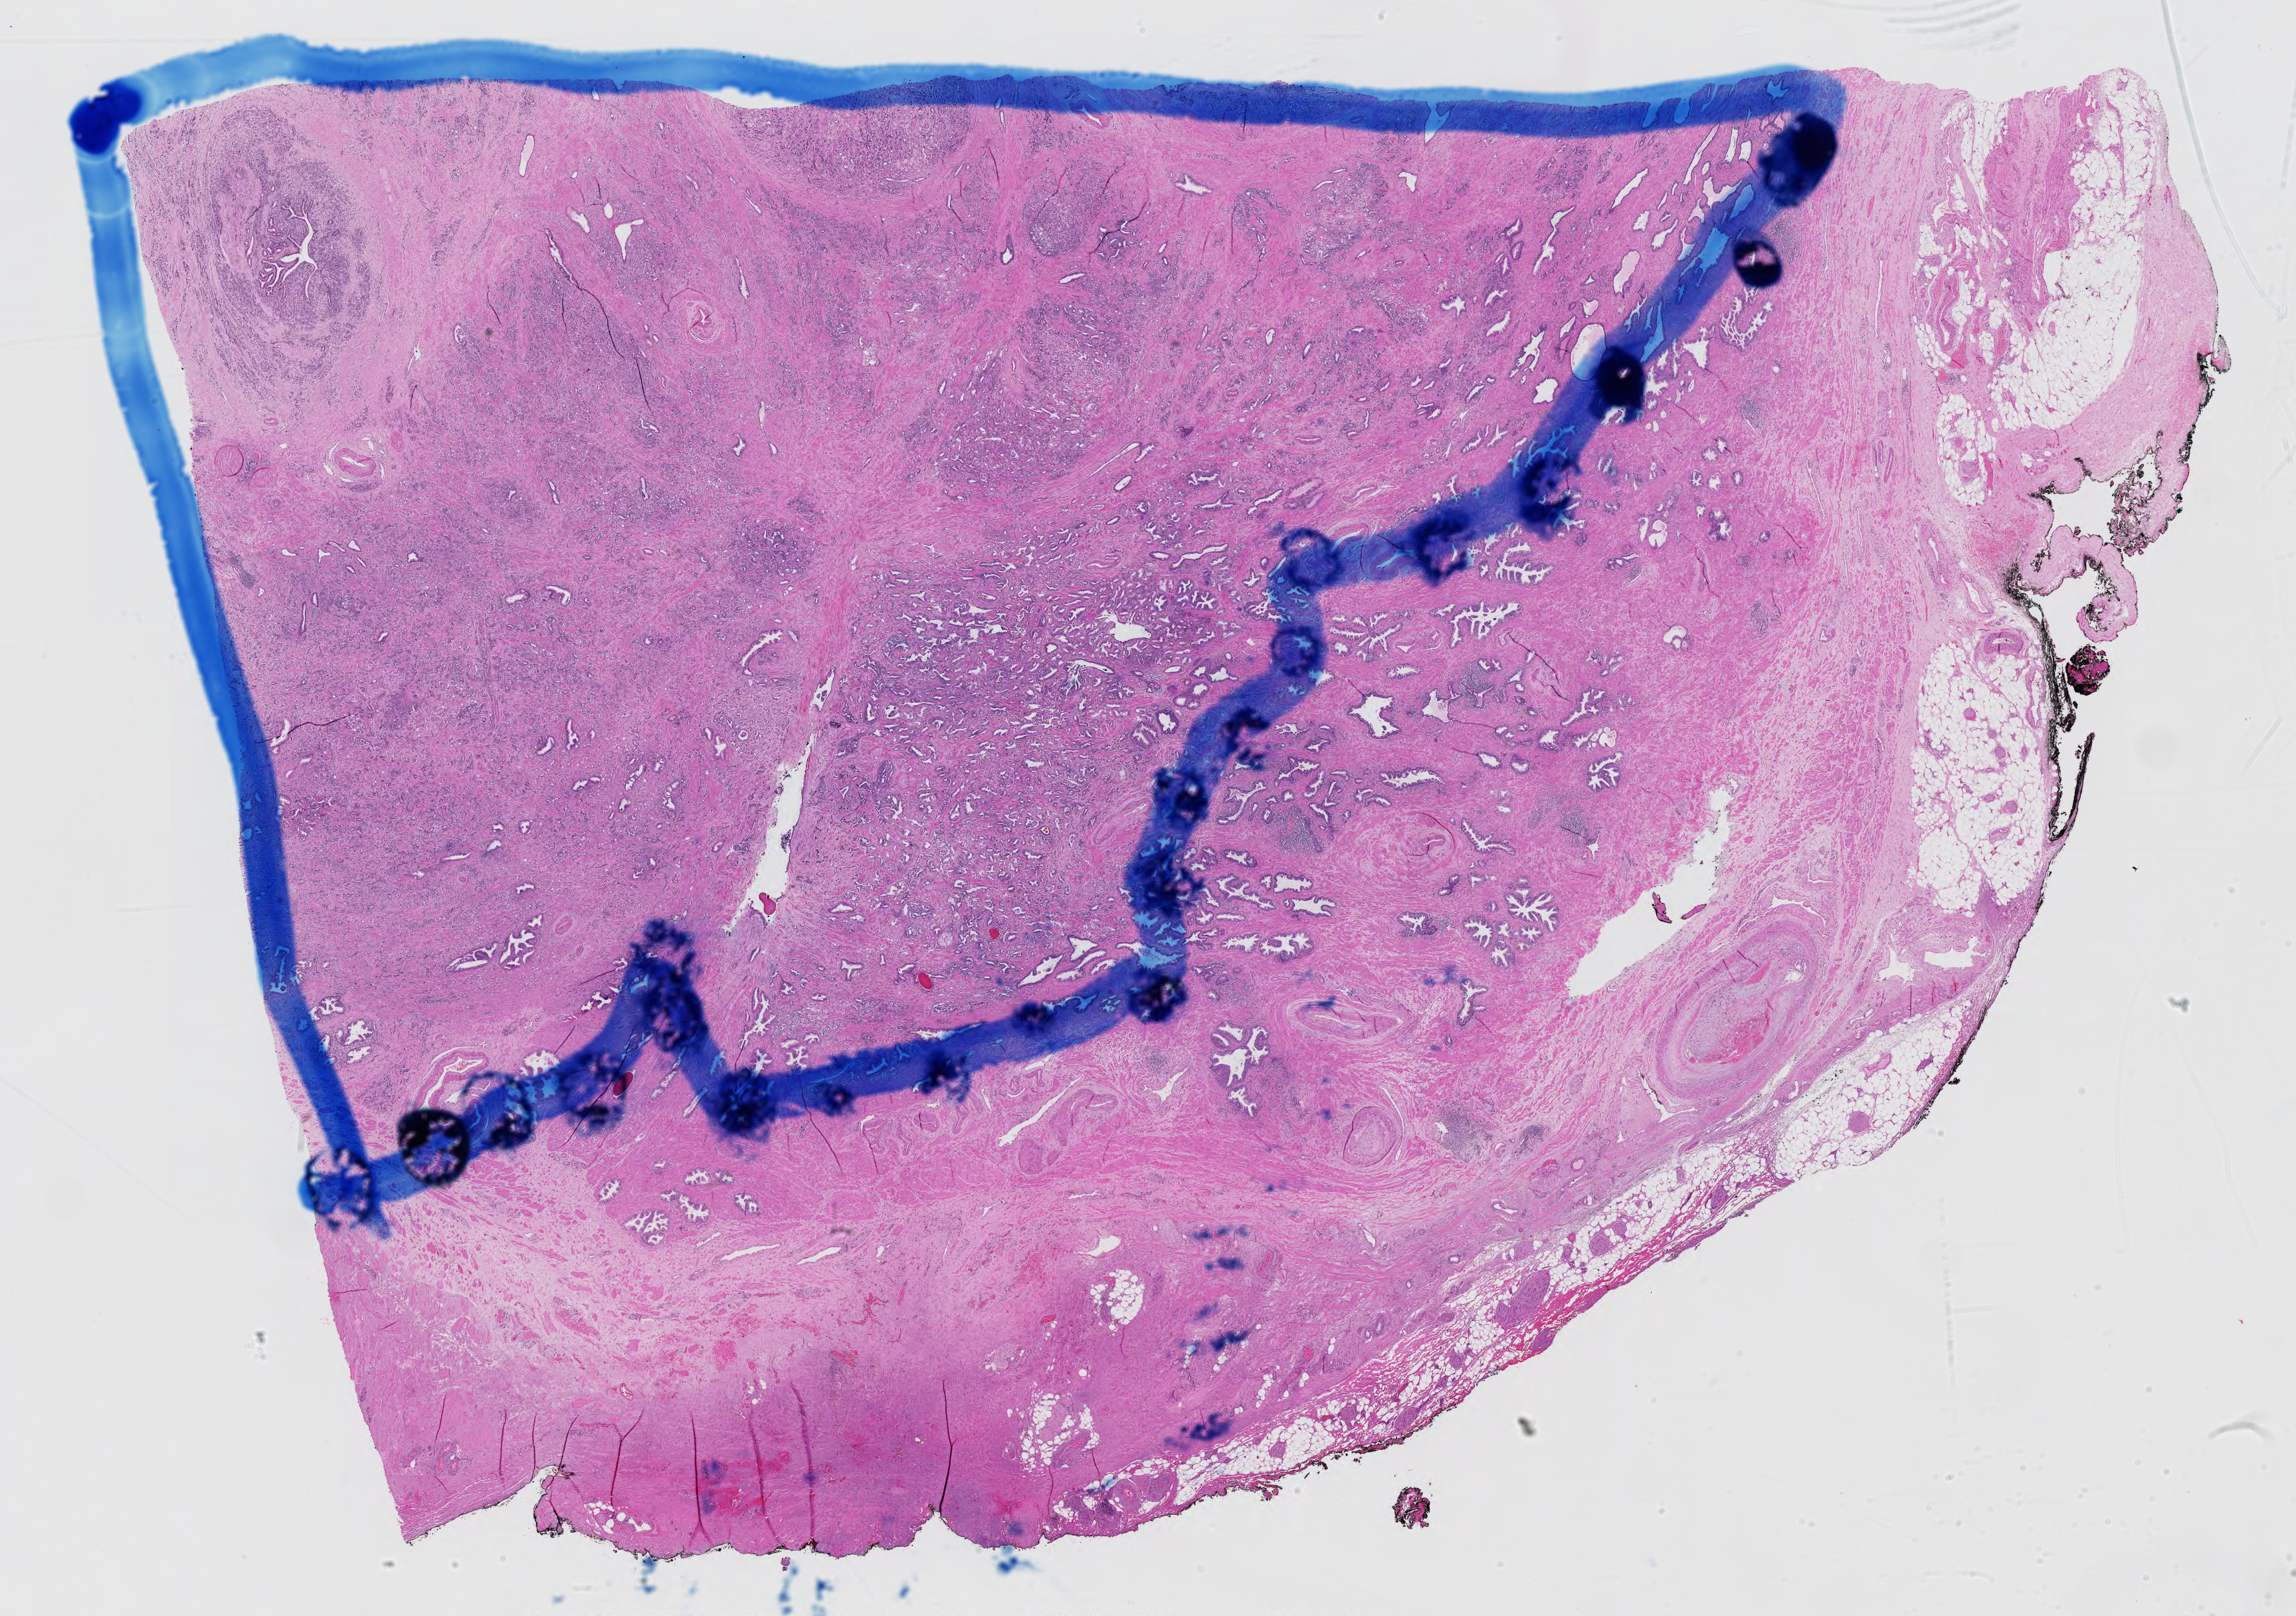
H&E-stained whole-slide image — whole scanned area (about 25.1 x 17.6 mm) shown as a low-resolution overview; formalin-fixed paraffin-embedded (FFPE) diagnostic section; prostate, primary tumour sample. Male patient; age at initial diagnosis 60 years. Gleason score: 9 (4+5).
Diagnosis: Adenocarcinoma, NOS (prostate gland). Laterality: bilateral. Lymph nodes positive (case pathology): 0 of 29 examined.